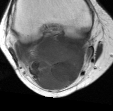
MRI of an extremity soft-tissue mass, one axial slice; MR volume resampled by the dataset authors to the PET/CT grid (not the native acquisition matrix); 113 × 111 image matrix, field of view 110 × 108 mm. Female patient. From the clinical record (not read from this slice): histological type: liposarcoma; site of the primary tumour: right thigh.
Structures marked on this image (expert contour drawn on MRI and transferred to this co-registered scan by the dataset authors):
- gross tumour volume (mass): bounding box <22,30,93,91> (left, top, right, bottom; pixels)